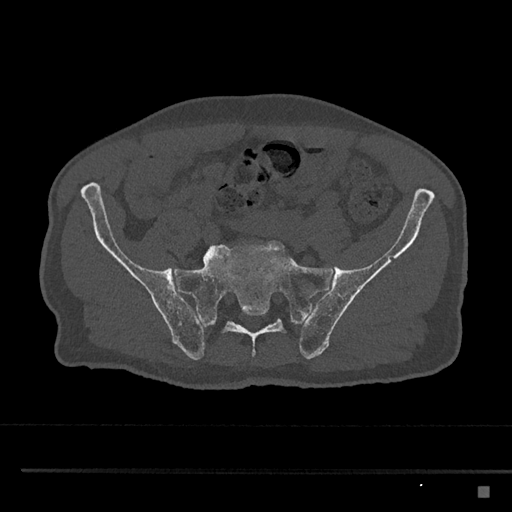
CT including the spine, one axial slice; slice 518 of 797 in the series (ordered by position); reconstruction kernel Br40s/3; 120 kVp; bone window (W 1800 / L 400 HU); 0.5 mm slice thickness; 512 × 512 image matrix. Male patient, age 59 years. Case-level facts recorded for this patient, not image findings: primary cancer: prostate.
Structures marked on this image (semi-automatically segmented with operator editing):
- L5 vertebra: bounding box (x1, y1, x2, y2) in pixels: (203, 253, 210, 260)